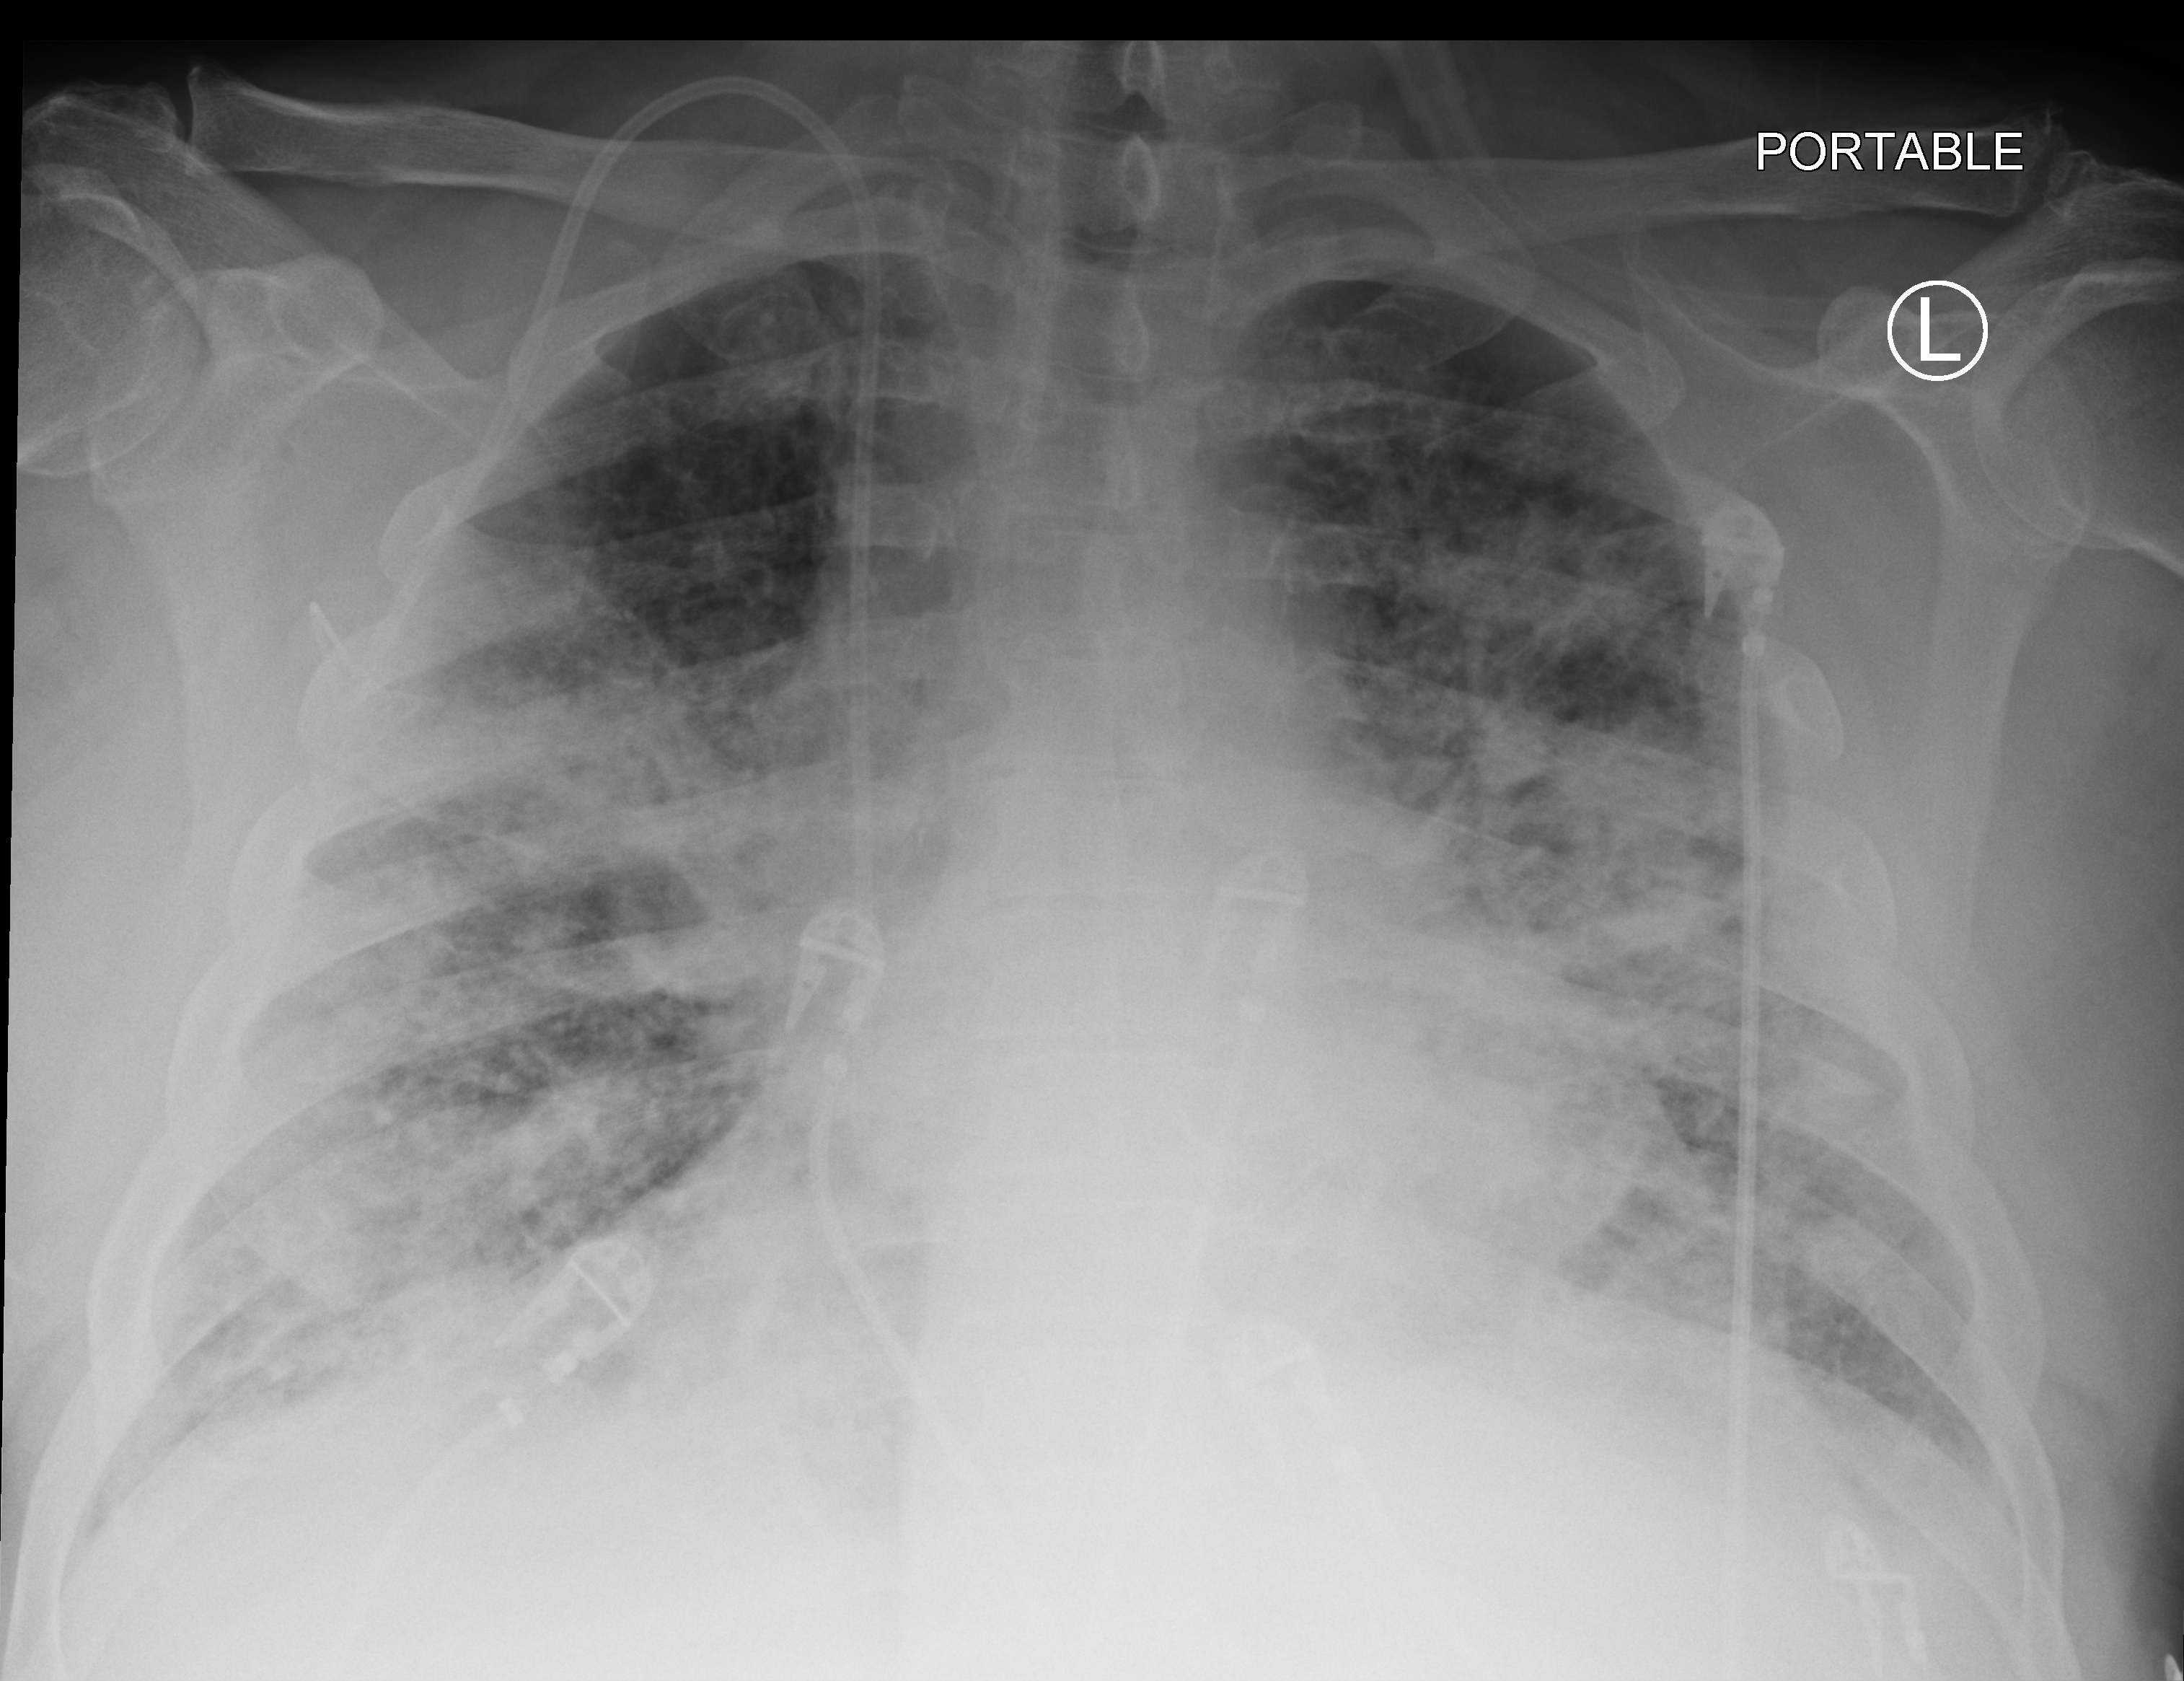
Bedside chest radiograph (computed radiography), anteroposterior (AP) projection. Male patient hospitalised with COVID-19, age 60–74 years.
From the hospital-stay record, not from the radiograph (when in the stay this image was taken is not recorded):
- admitted to intensive care during this hospital stay: no
- mechanically ventilated during this hospital stay: no